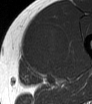
MRI of an extremity soft-tissue mass, one axial slice; position 33 of 62 along the scan axis; MR volume resampled by the dataset authors to the PET/CT grid (not the native acquisition matrix); 92 × 104 image matrix, field of view 90 × 102 mm. Male patient. Case-level facts recorded for this patient, not image findings: histological type: mixoid liposarcoma; grade: low; site of the primary tumour: left thigh.
Structures marked on this image (expert contour drawn on MRI and transferred to this co-registered scan by the dataset authors):
- gross tumour volume (mass): bounding box [x1, y1, x2, y2] px = [21, 22, 70, 77]